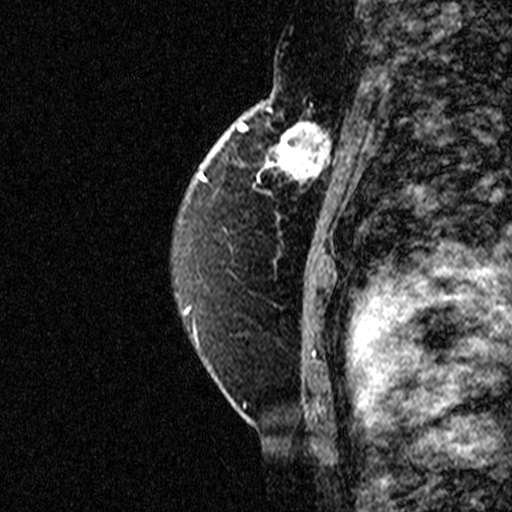
Breast MRI (dynamic contrast-enhanced), one sagittal slice. Dynamic contrast-enhanced study with each time point stored as its own series, time point 2 of 3 at this slice position (early post-contrast, ordered by acquisition time). 1.5 T. TE 4.5 ms, TR 11 ms. 512 × 512 image matrix, field of view 200 × 200 mm. Female patient, age 49 years. Case-level facts recorded for this patient, not image findings: setting: breast cancer imaged before/during neoadjuvant chemotherapy; receptor status: triple-negative.
Annotated regions visible in this slice (semi-automatic segmentation, software-assisted and operator-edited):
- analysis volume of interest (the breast-tissue region the enhancement analysis was run in; not a lesion): bounding box (x1, y1, x2, y2) in pixels: (254, 112, 347, 207)
- tumour enhancement mask (voxels above the 90 % enhancement threshold inside the analysis volume of interest): (257, 112, 347, 207)